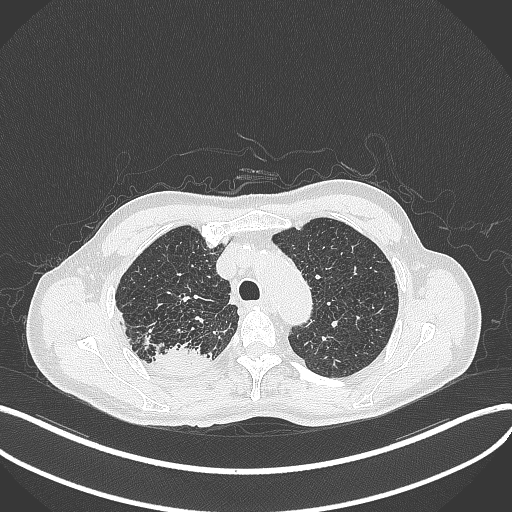
Chest CT, one axial slice; slice 344 of 428 in the series (ordered by position); reconstruction kernel B70f; lung window (W 1500 / L -600 HU); 1 mm slice thickness; 512 × 512 image matrix, field of view 400 × 400 mm. Patient: male, 79 years. From the clinical record (not read from this slice): clinical TNM (as recorded): T3 N0 M0.
Annotated regions visible in this slice (bounding box drawn by a radiologist):
- lung tumour (recorded histology: adenocarcinoma): box from (x=150, y=338) to (x=209, y=369) px